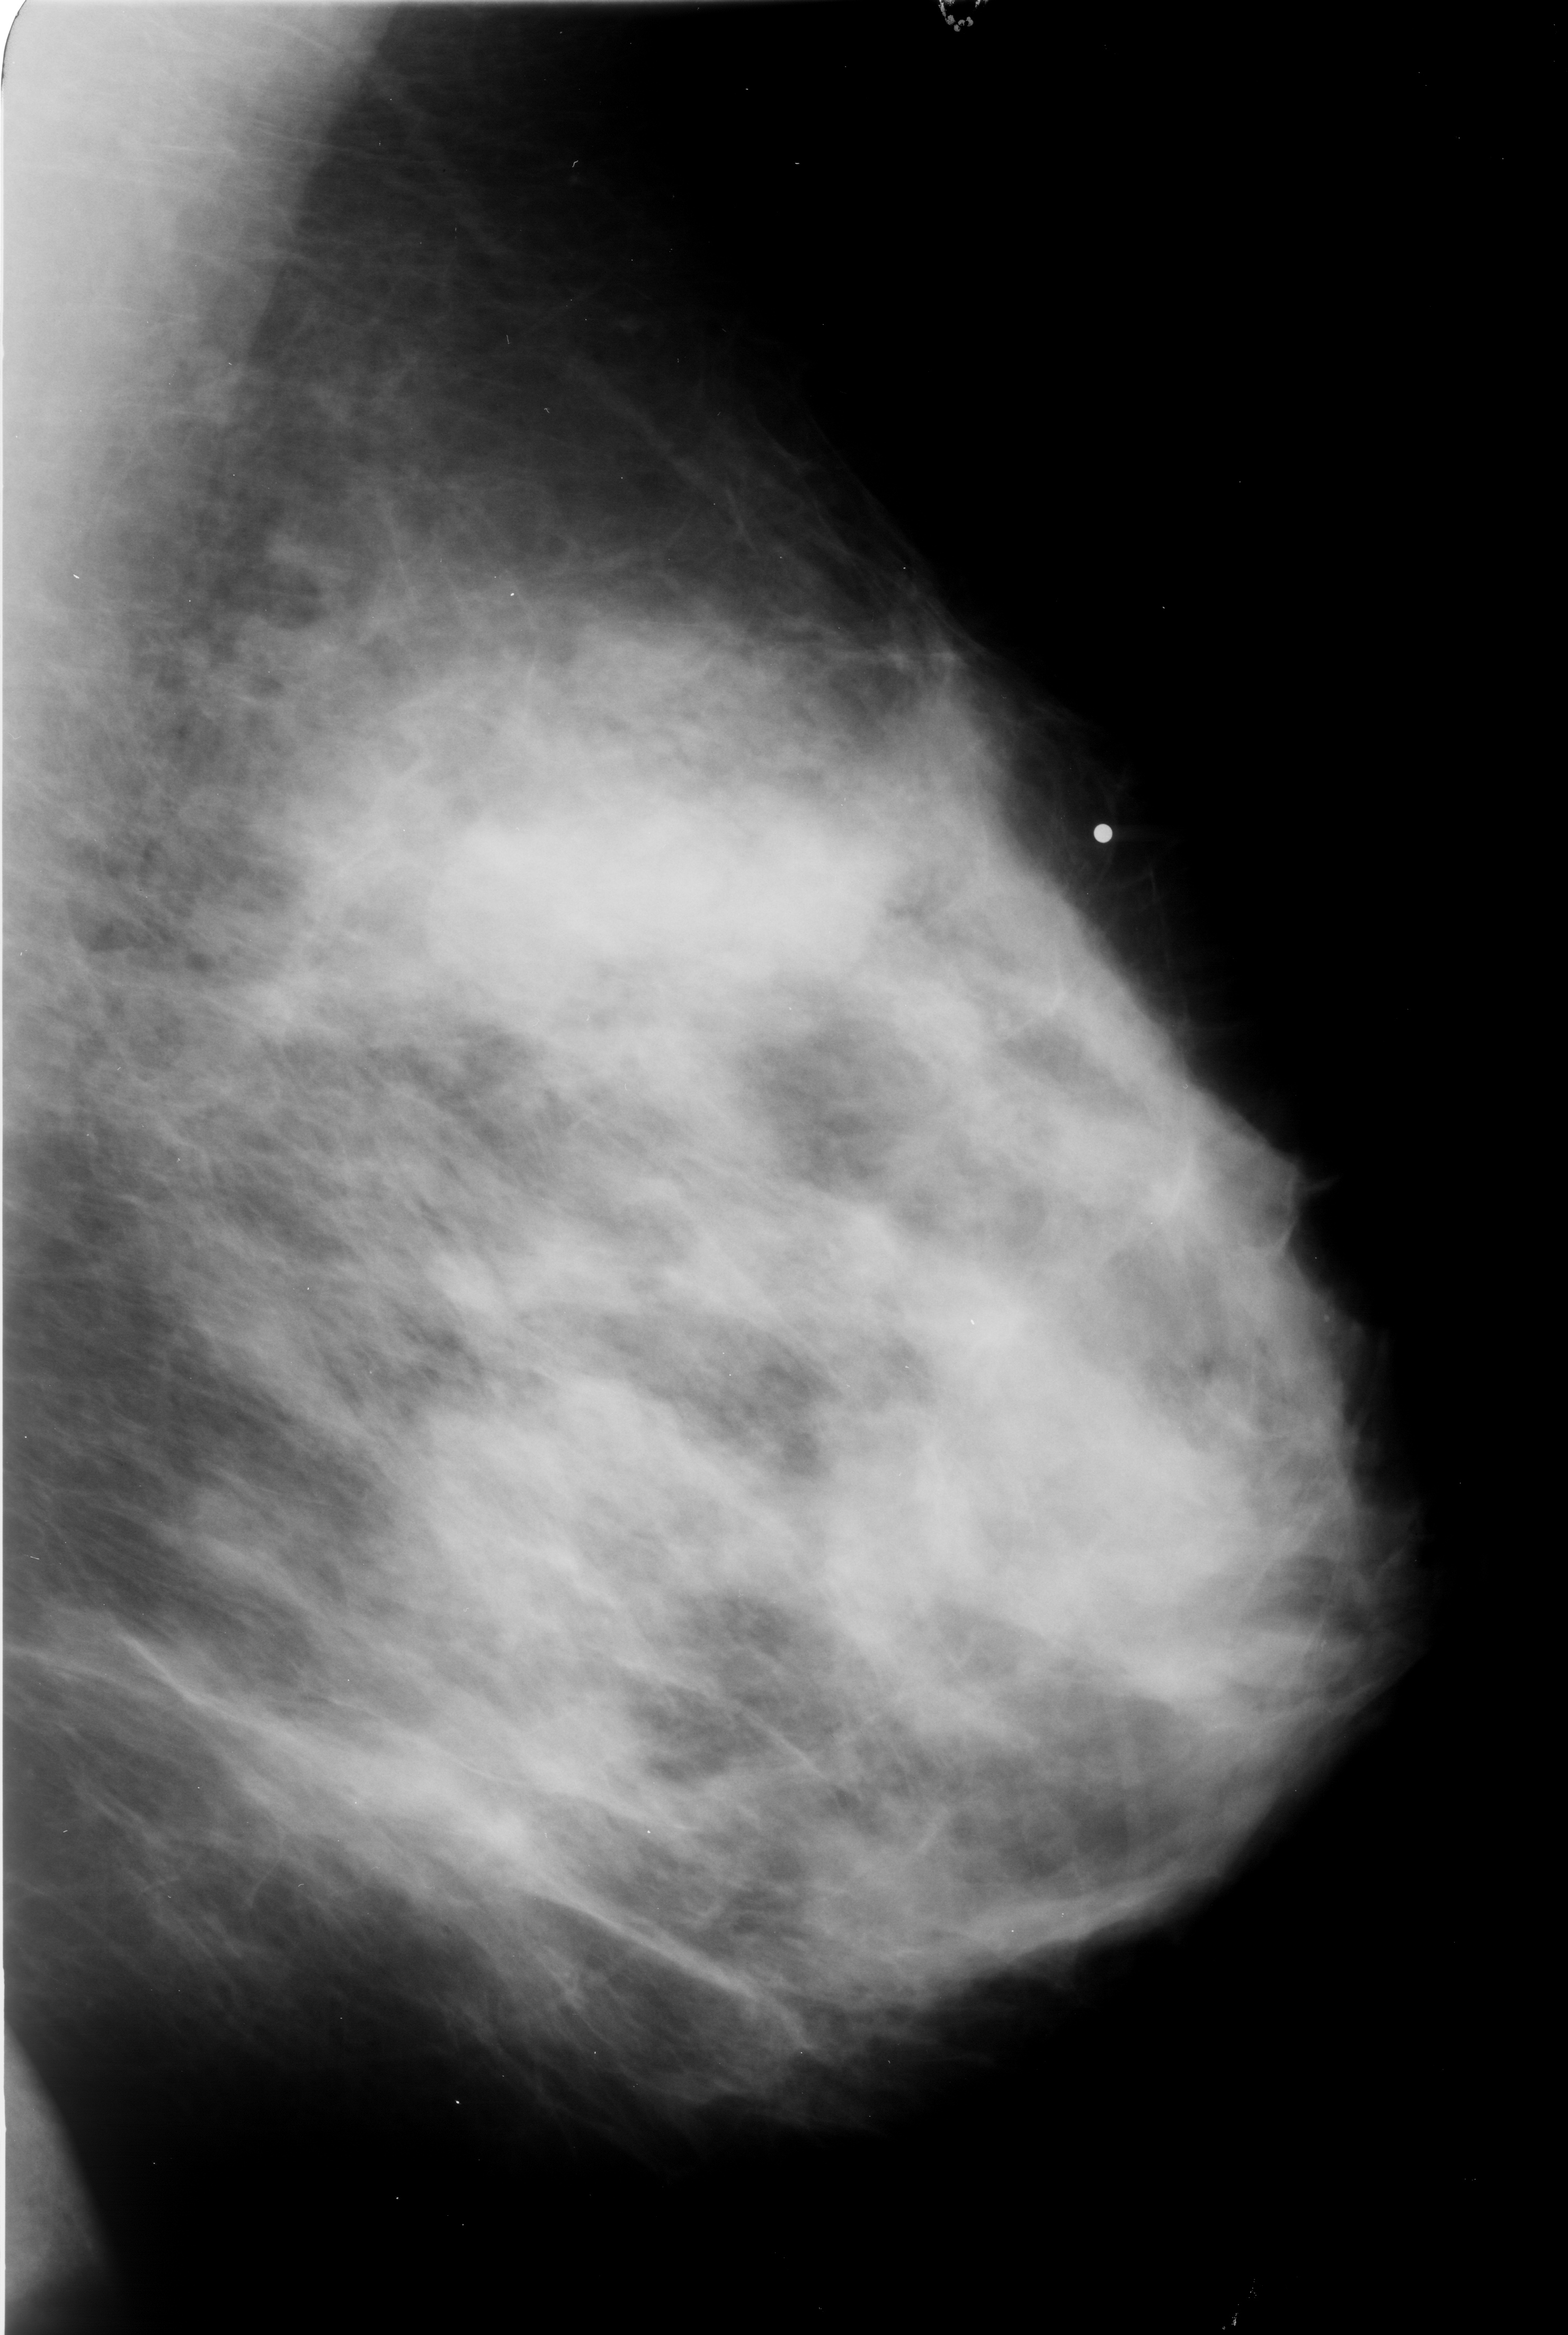
Mammogram (digitized film), left breast, mediolateral oblique (MLO) view.
Finding: mass, shape lobulated / irregular, margins obscured / ill defined; BI-RADS assessment category 4; subtlety rating 4 on a 1 (subtle) to 5 (obvious) scale; pathology (as recorded): malignant.